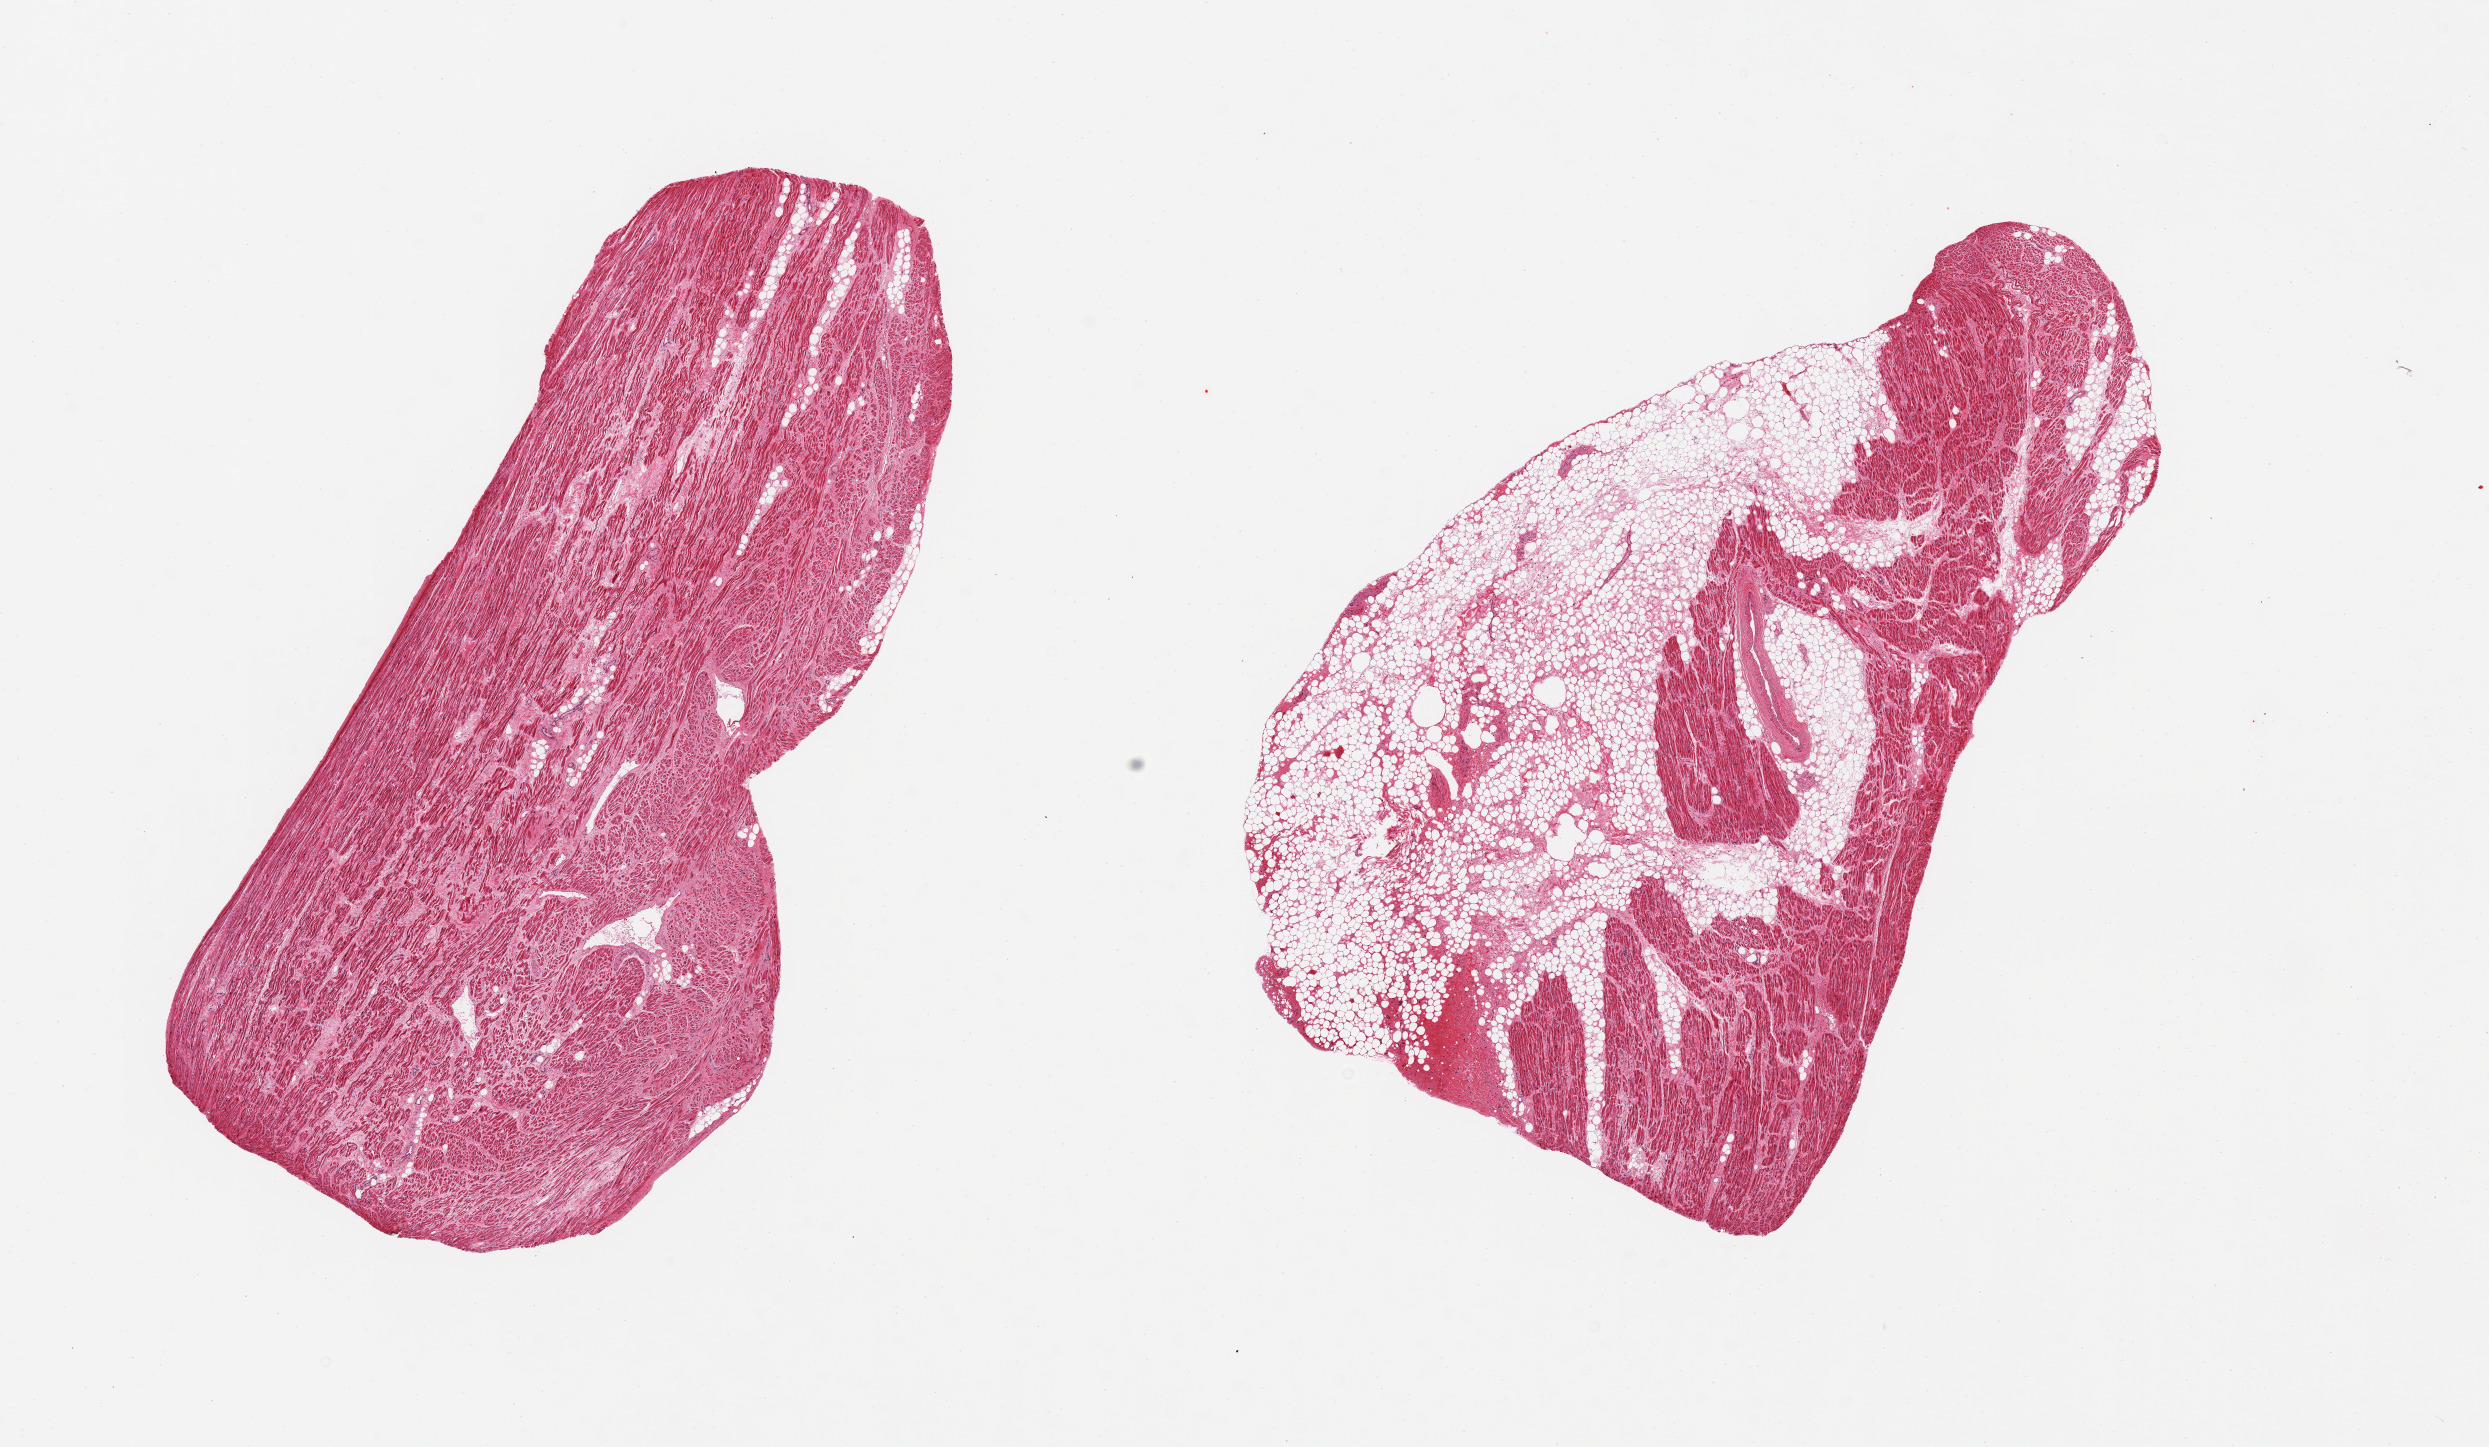
Whole-slide image, H&E stain — shown as a low-resolution overview of the whole scanned area (about 19.7 x 11.4 mm, acquisition: 20x scan), PAXgene-fixed paraffin-embedded (PFPE) section, target tissue: auricular appendage, tissue donor sample. Male donor.
Pathologist's review note for this sample: 2 pieces, 1 piece is 60% fat.